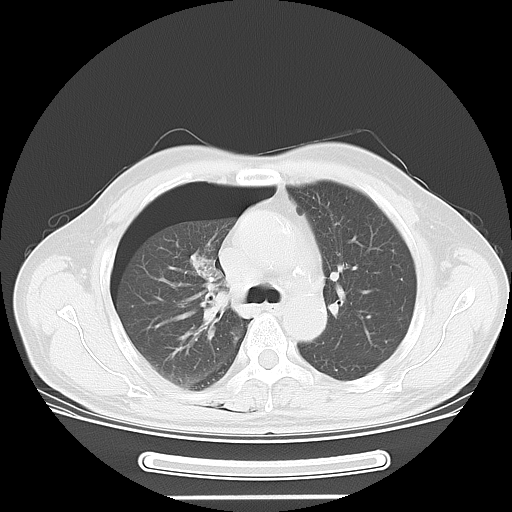
Chest CT, one axial slice; slice 39 of 57 in the series (ordered by position); reconstruction kernel LUNG; 120 kVp; lung window (W 1500 / L -600 HU); 5 mm slice thickness; 512 × 512 image matrix. Male patient, age 61 years. Case-level facts recorded for this patient, not image findings: clinical TNM (as recorded): T1c N3 M1b.
Outlined on this slice (rectangle marked by the reading radiologist):
- lung tumour (recorded histology: adenocarcinoma): bounding box (x1, y1, x2, y2) in pixels: (188, 239, 237, 343)